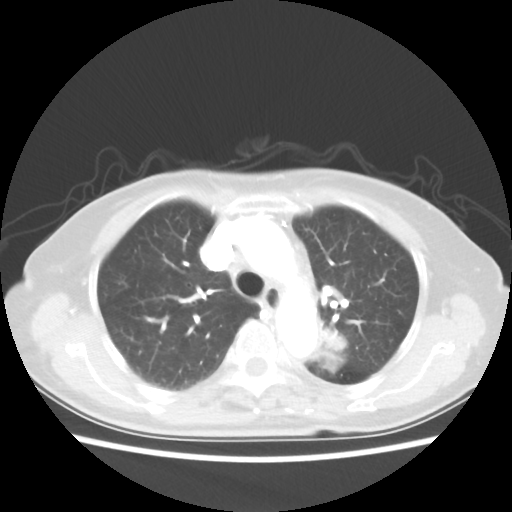
Chest CT, one axial slice. Position 34 of 50 along the scan axis. Reconstruction kernel STANDARD. 80 kVp. Lung window (W 1500 / L -600 HU). 512 × 512 image matrix, field of view 335 × 335 mm. Patient: female, 81 years. From the clinical record (not read from this slice): clinical TNM (as recorded): T2 N0 M1a.
Outlined on this slice (bounding box drawn by a radiologist):
- lung tumour (recorded histology: squamous cell carcinoma): box from (x=316, y=327) to (x=348, y=368) px